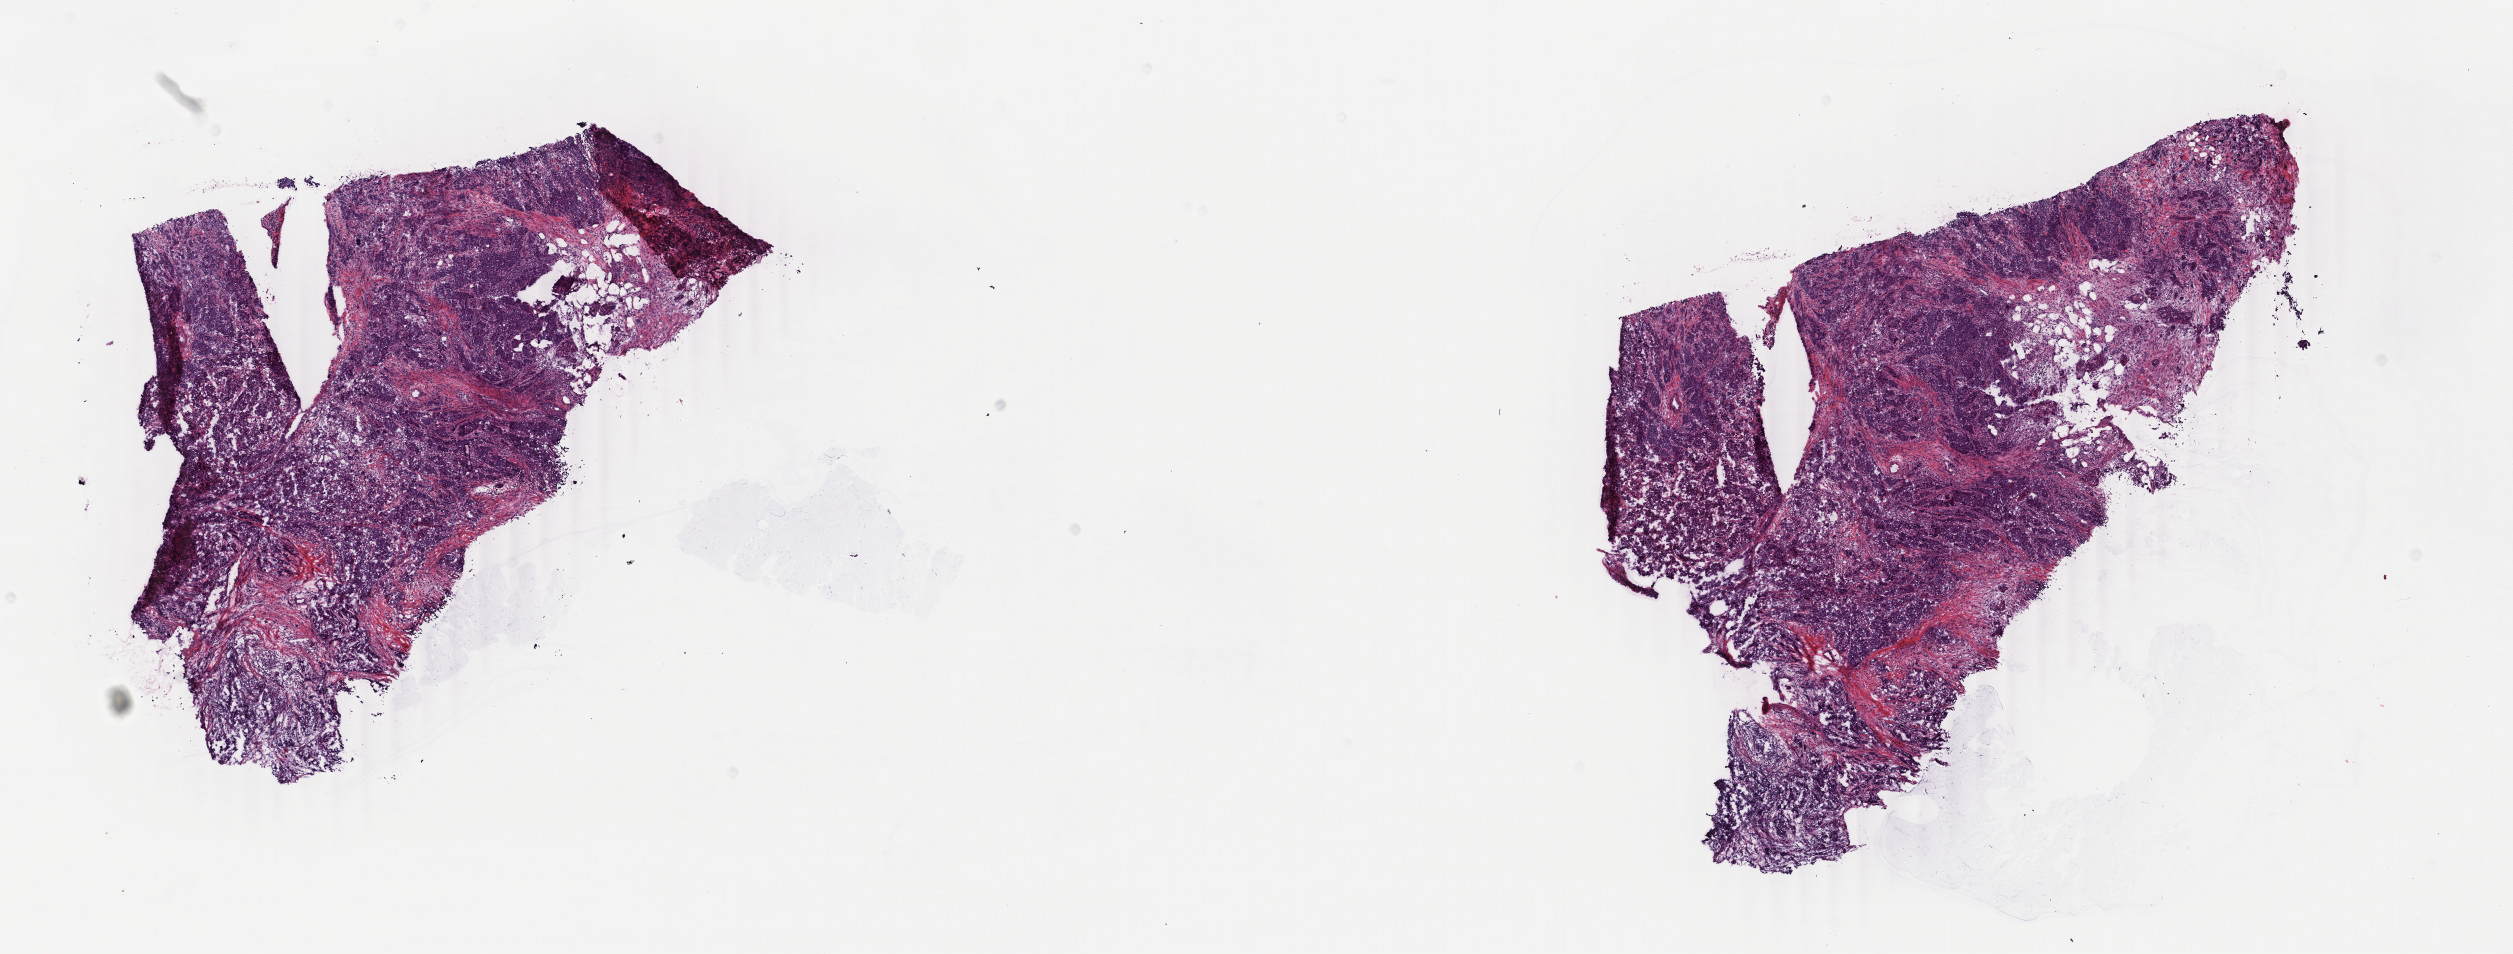
H&E-stained whole-slide image — whole scanned area (about 20.0 x 7.6 mm, from a 40x scan) shown as a low-resolution overview, frozen section, sample: primary tumour, breast. Female, age 40 years at initial diagnosis. Slide review estimates, as recorded: tumour cells 70%, tumour nuclei 75%, normal cells 0%, stromal cells 23%, necrosis 7%. Infiltration values recorded for this section: lymphocyte infiltration 25%, monocyte infiltration 10%, neutrophil infiltration 10%.
• histologic diagnosis: Infiltrating duct carcinoma, NOS
• AJCC pathologic stage: IIA (6th edition)